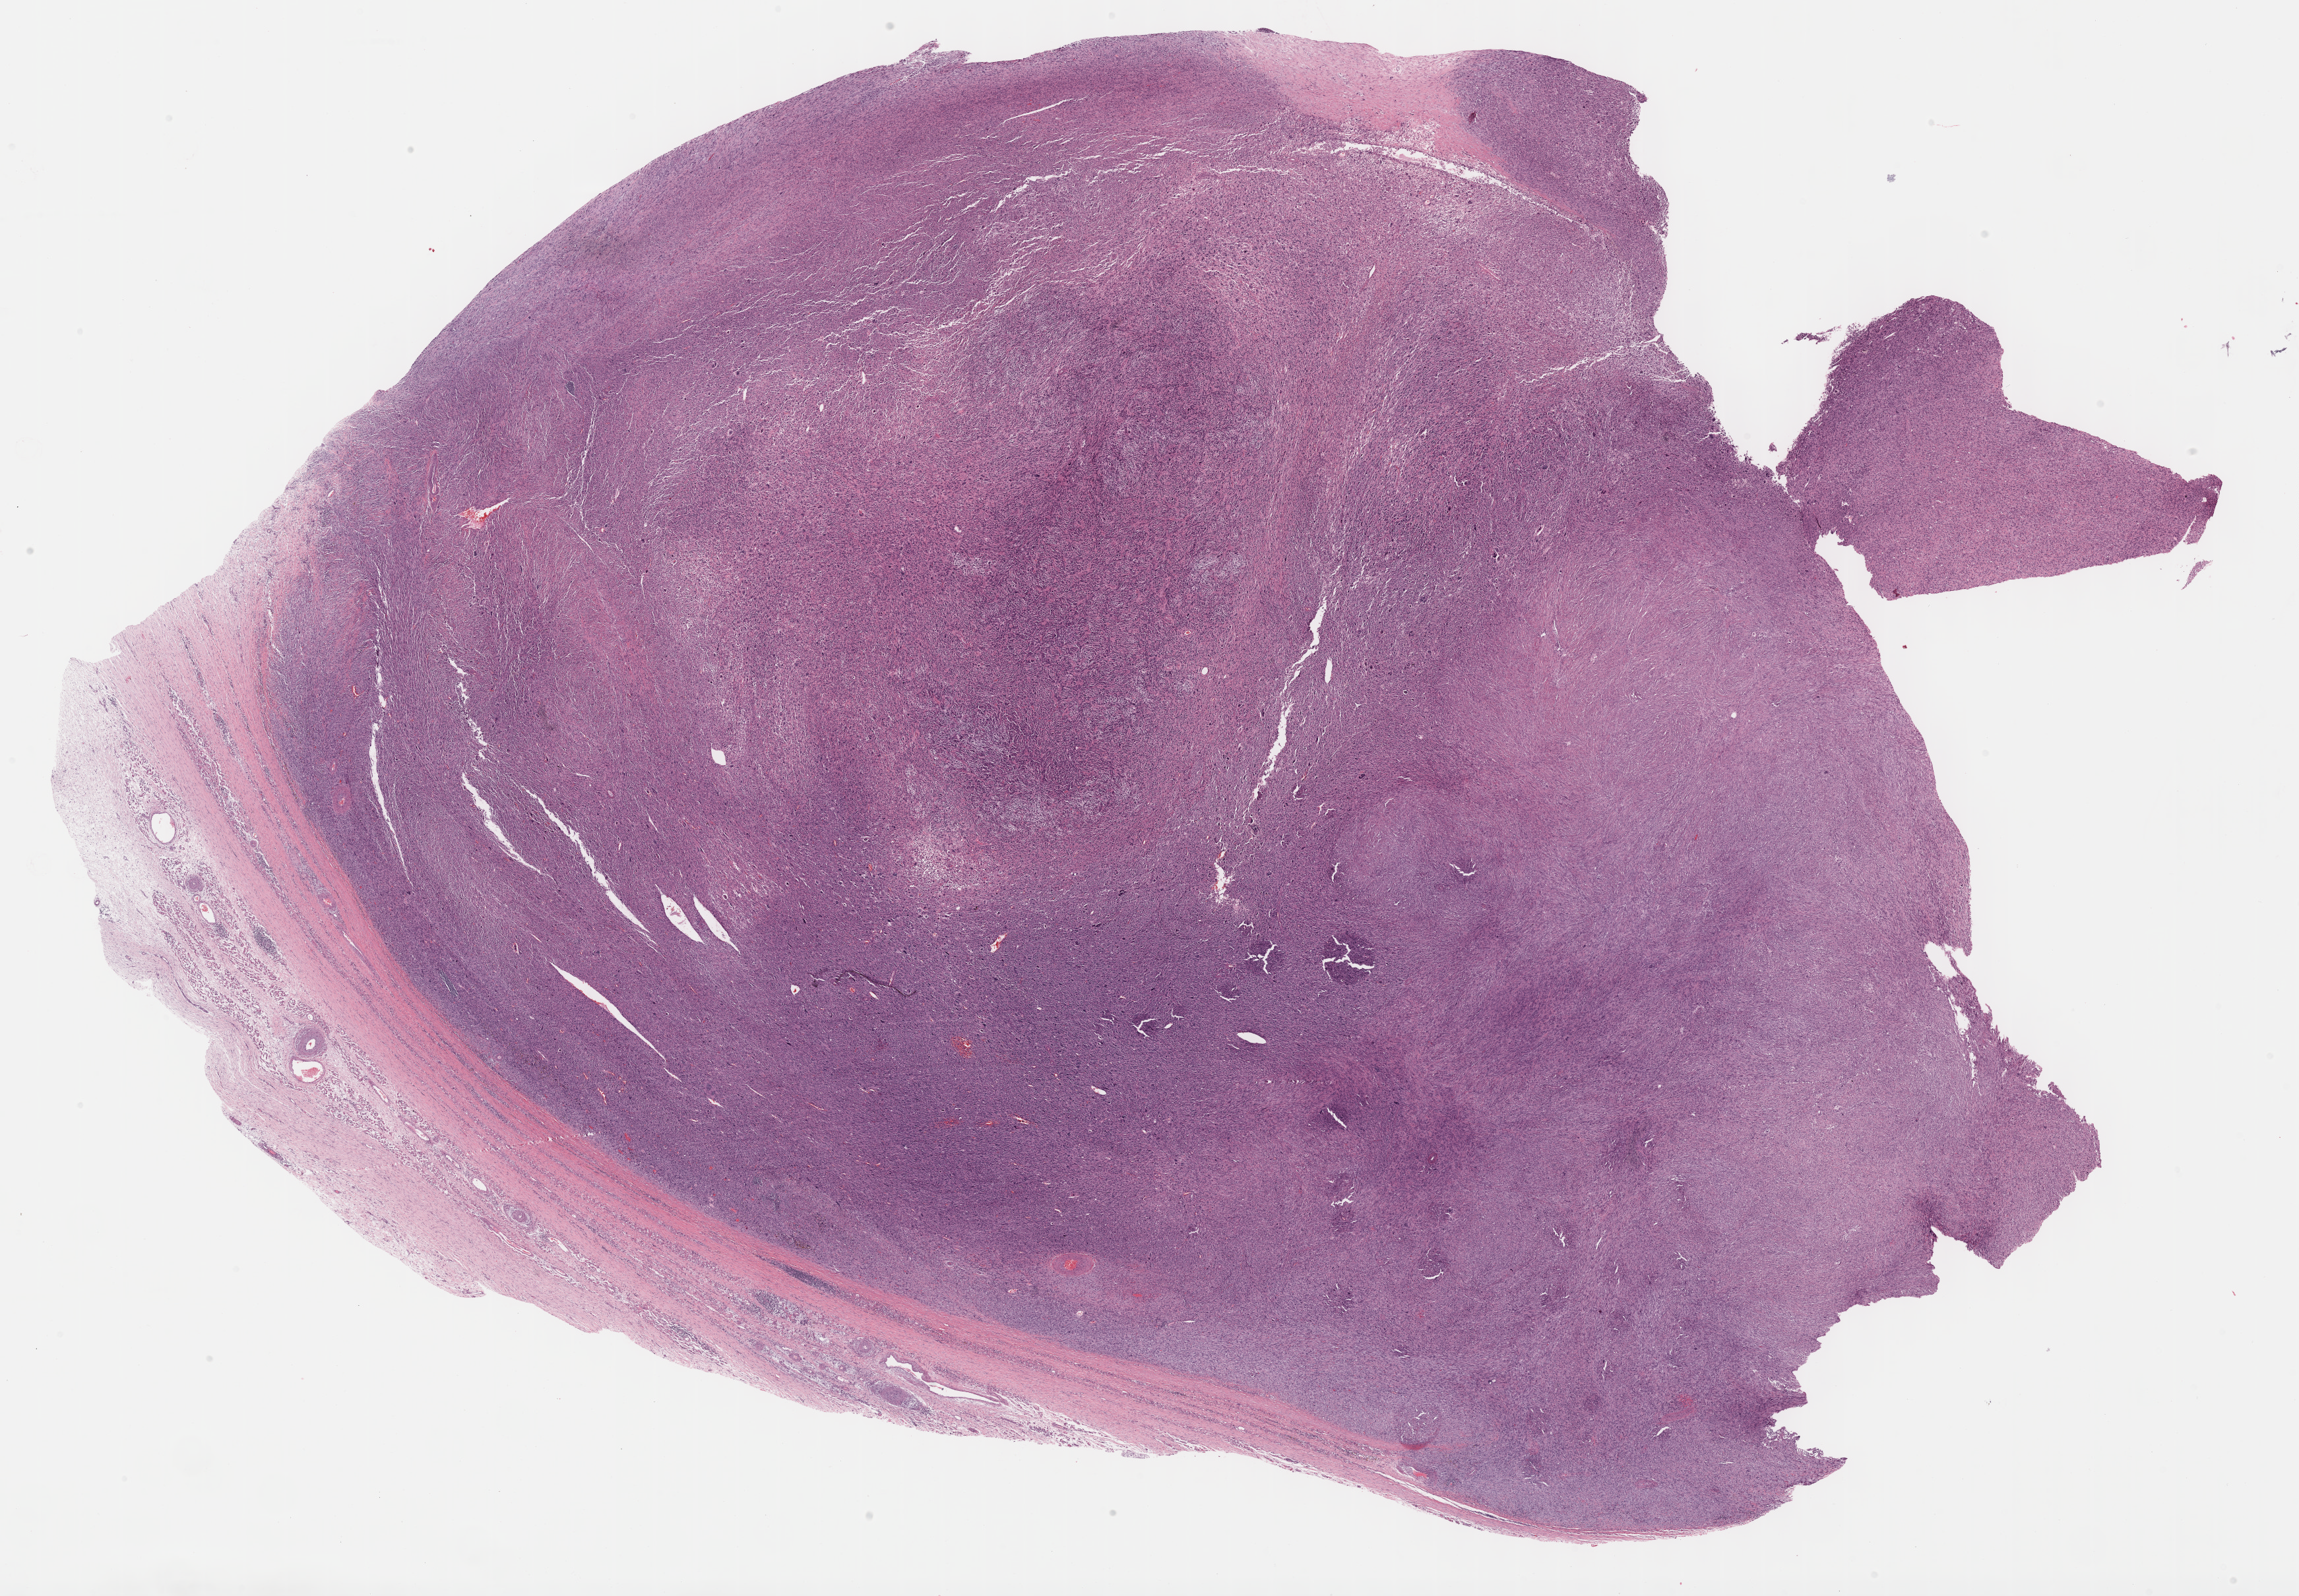
Hematoxylin and eosin (H&E) stained whole-slide image, shown as a low-resolution overview of the whole scanned area (about 28.2 x 19.6 mm, slide scanned at 40x). Formalin-fixed paraffin-embedded (FFPE) diagnostic section. Connective, subcutaneous and other soft tissues, primary tumour sample. Patient: male, age at initial diagnosis 79 years.
Diagnosis: Malignant fibrous histiocytoma (connective, subcutaneous and other soft tissues of lower limb and hip).